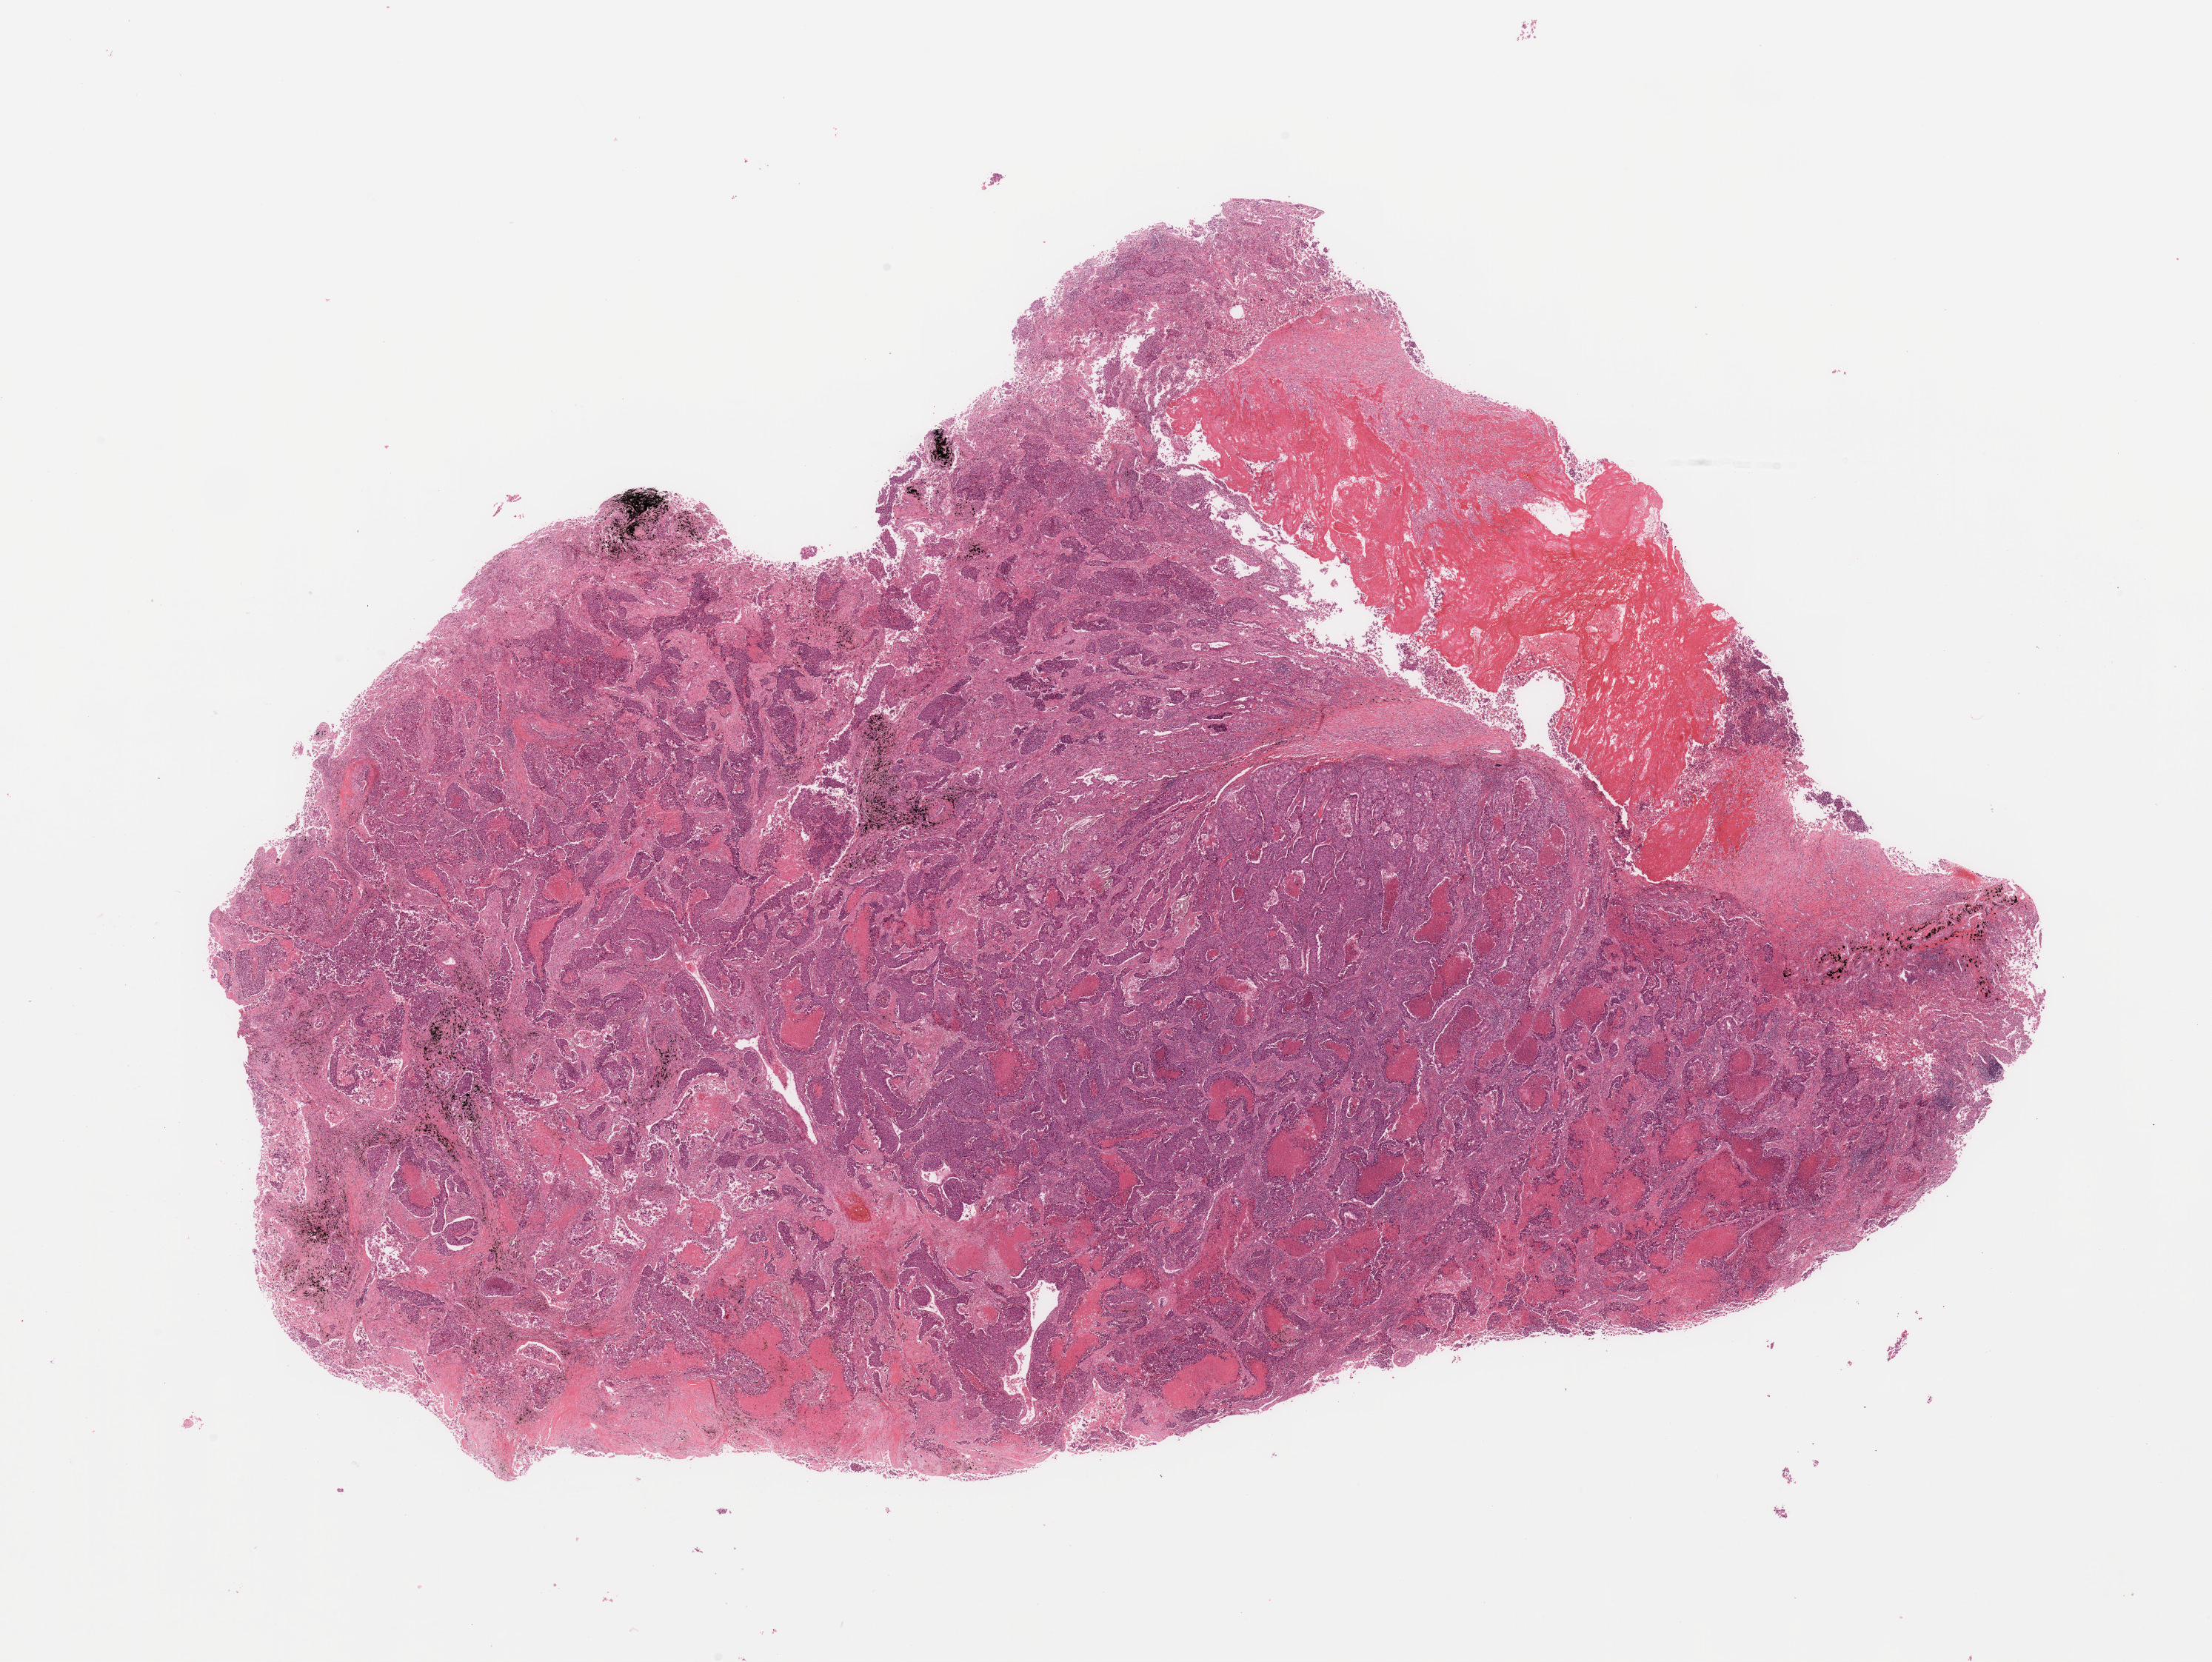
Digitized Hematoxylin and eosin (H&E) stained tissue section (whole slide) — a low-resolution overview of the entire scanned area, about 23.6 x 17.7 mm, tumour tissue sample, lung. 56-year-old male patient. Histologic grade: G3 (poorly differentiated).
• primary tumour site (as recorded): left upper lobe
• diagnosis: Adenocarcinoma, NOS
• AJCC pathologic stage: IB